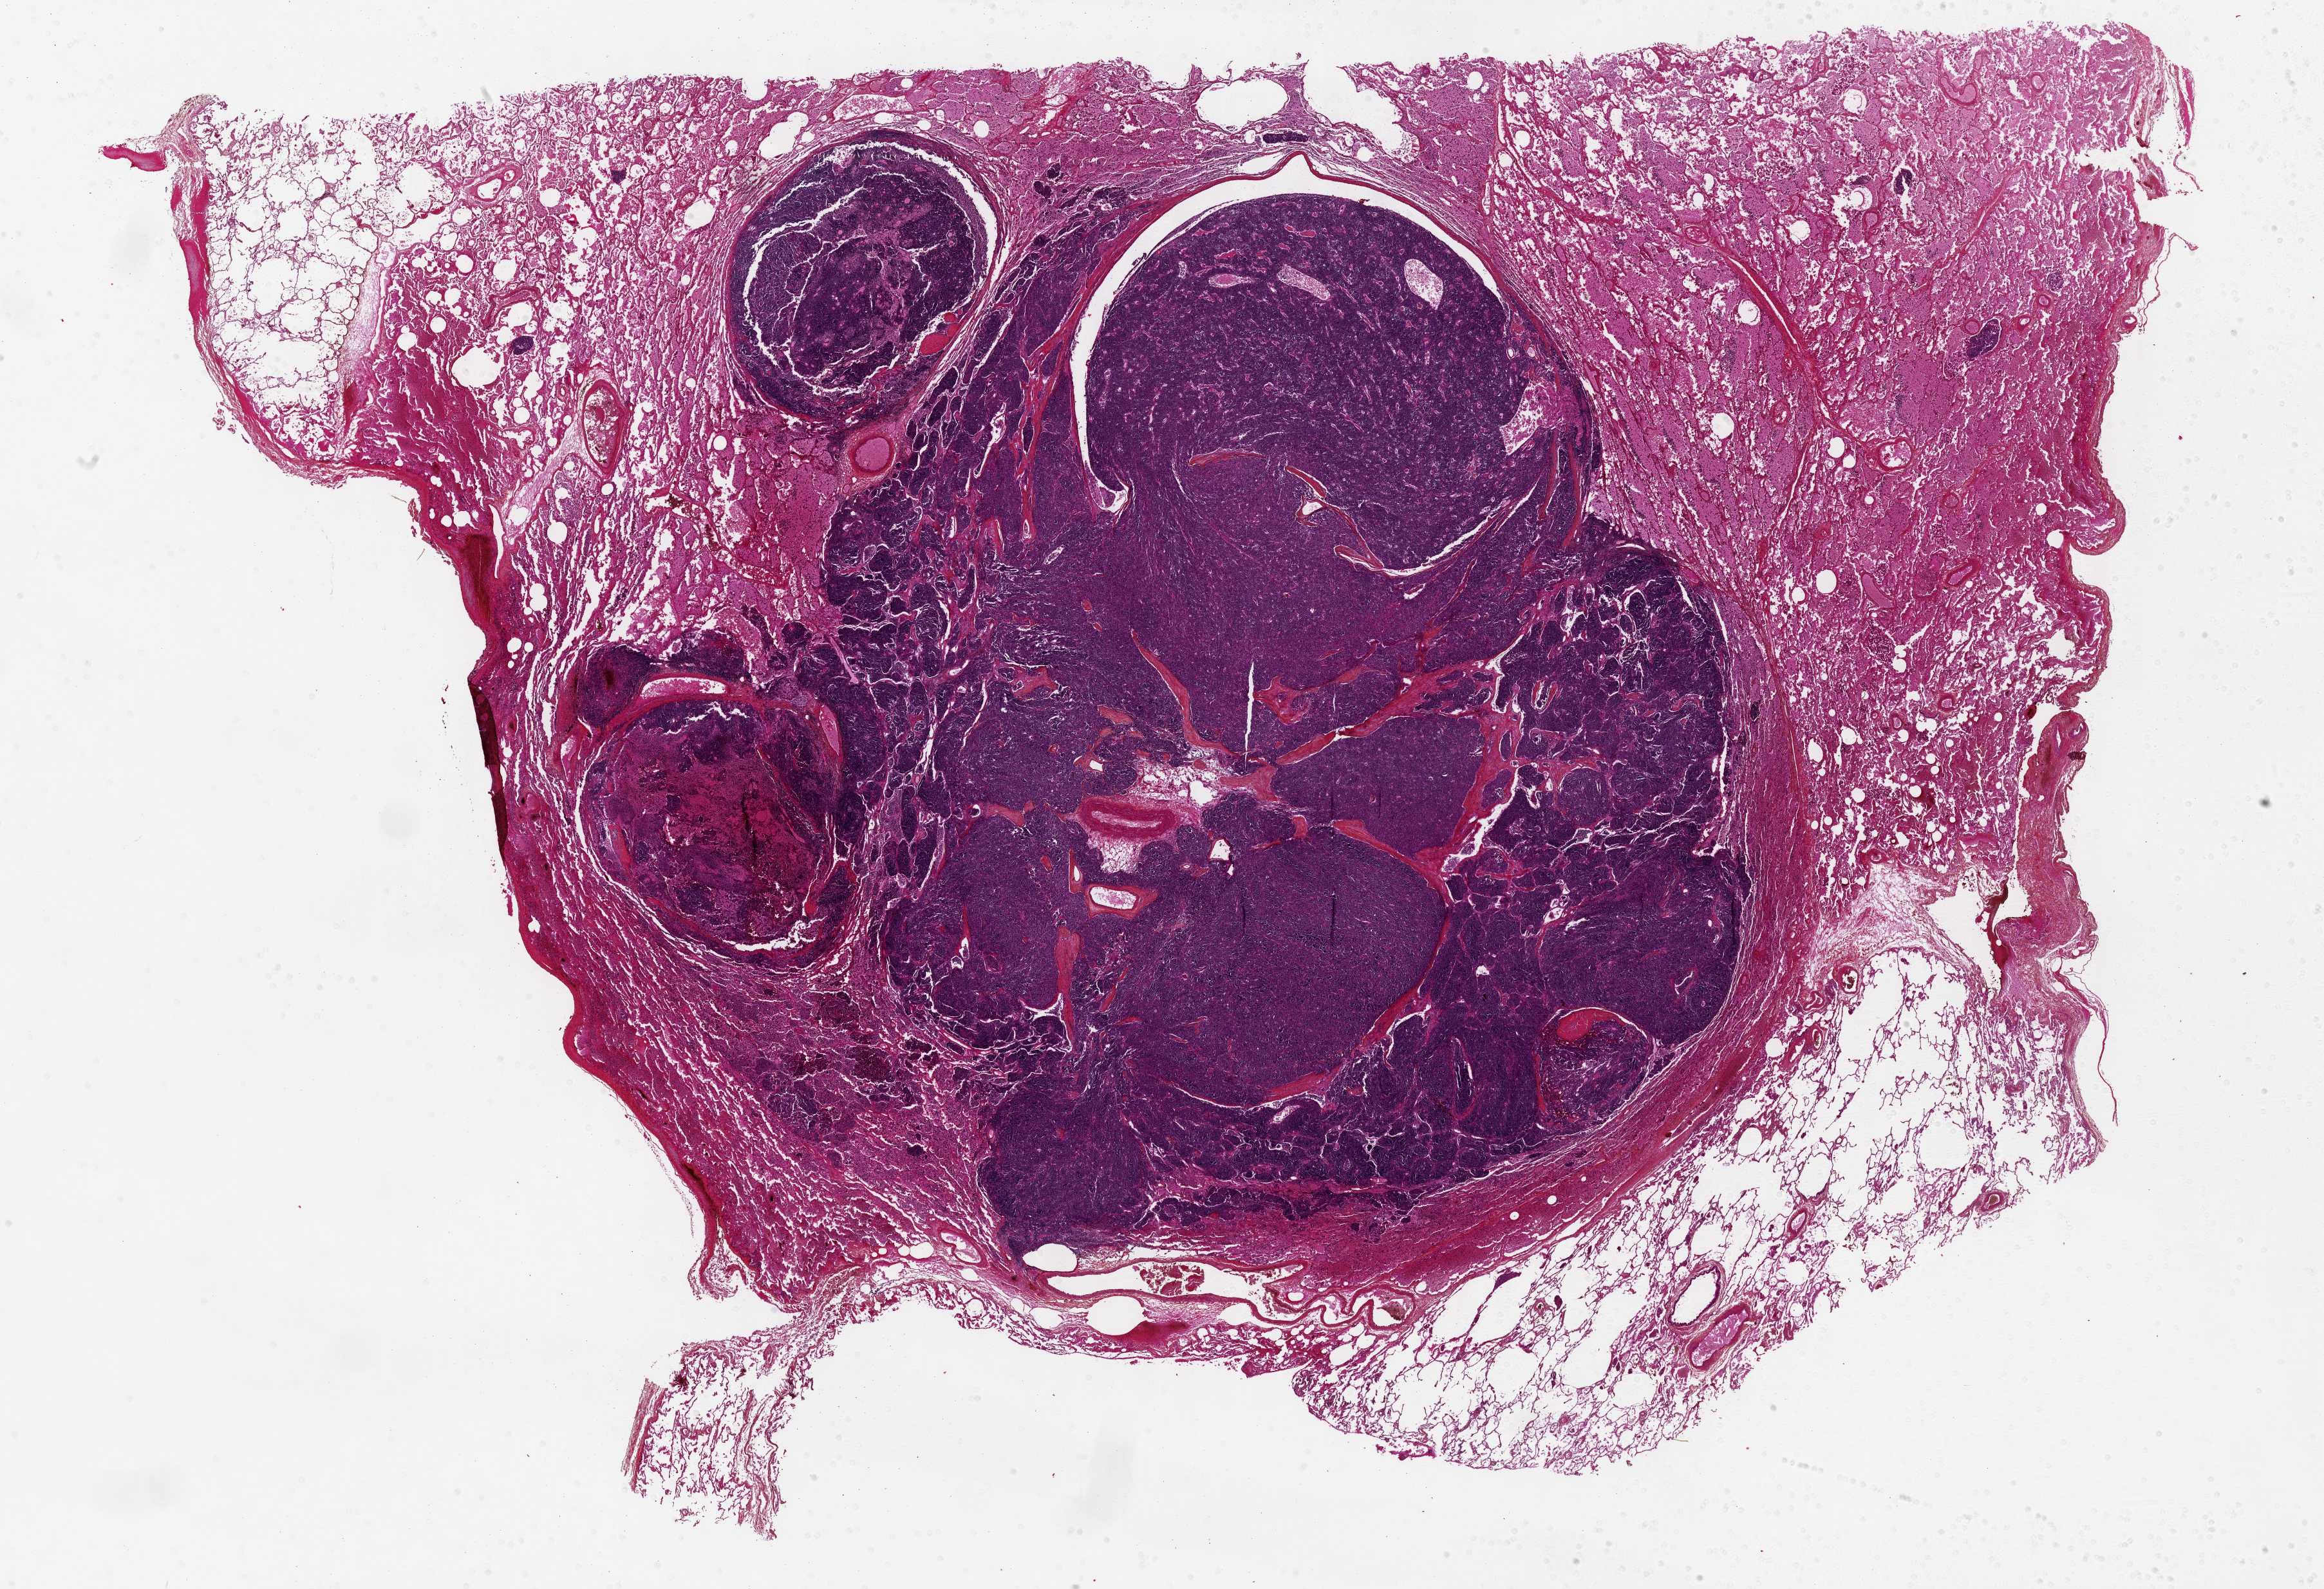
Whole-slide histology image, H&E-stained, shown as a low-resolution overview of the whole scanned area (about 29.2 x 20.0 mm, from a 40x scan); formalin-fixed paraffin-embedded (FFPE) diagnostic section; thymus, primary tumour sample. Patient: male, age at initial diagnosis 64 years.
Diagnosis: Thymoma, type B3, malignant.